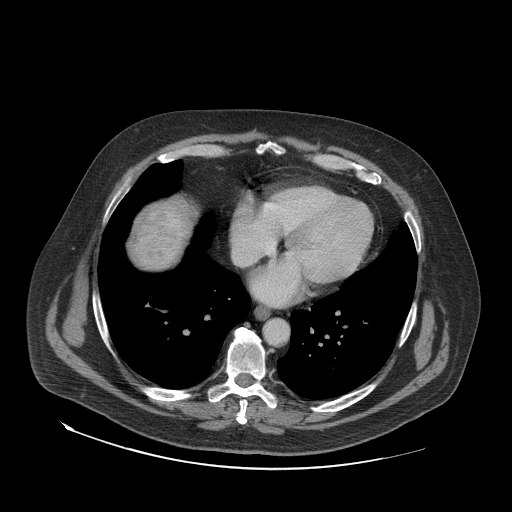
Contrast-enhanced abdominal CT (liver protocol), one axial slice; slice 74 of 79 in the series (ordered by position); reconstruction kernel STANDARD; 140 kVp; soft-tissue window (W 400 / L 40 HU); 2.5 mm slice thickness; 512 × 512 image matrix, field of view 480 × 480 mm. Case-level facts recorded for this patient, not image findings: diagnosis: hepatocellular carcinoma (patient treated with transarterial chemoembolisation; whether this scan precedes or follows treatment is not stated here); TNM stage (as recorded): Stage-IVA; Child-Pugh class: A; tumour differentiation: well differentiated; tumour nodularity: multinodular.
Structures marked on this image (semi-automatically segmented with operator editing):
- liver parenchyma outside the tumour (the mass and vessels are separate outlines, so this box may not span the whole liver): box from (x=132, y=204) to (x=190, y=268) px
- mass: (x=133, y=205)–(x=186, y=265)